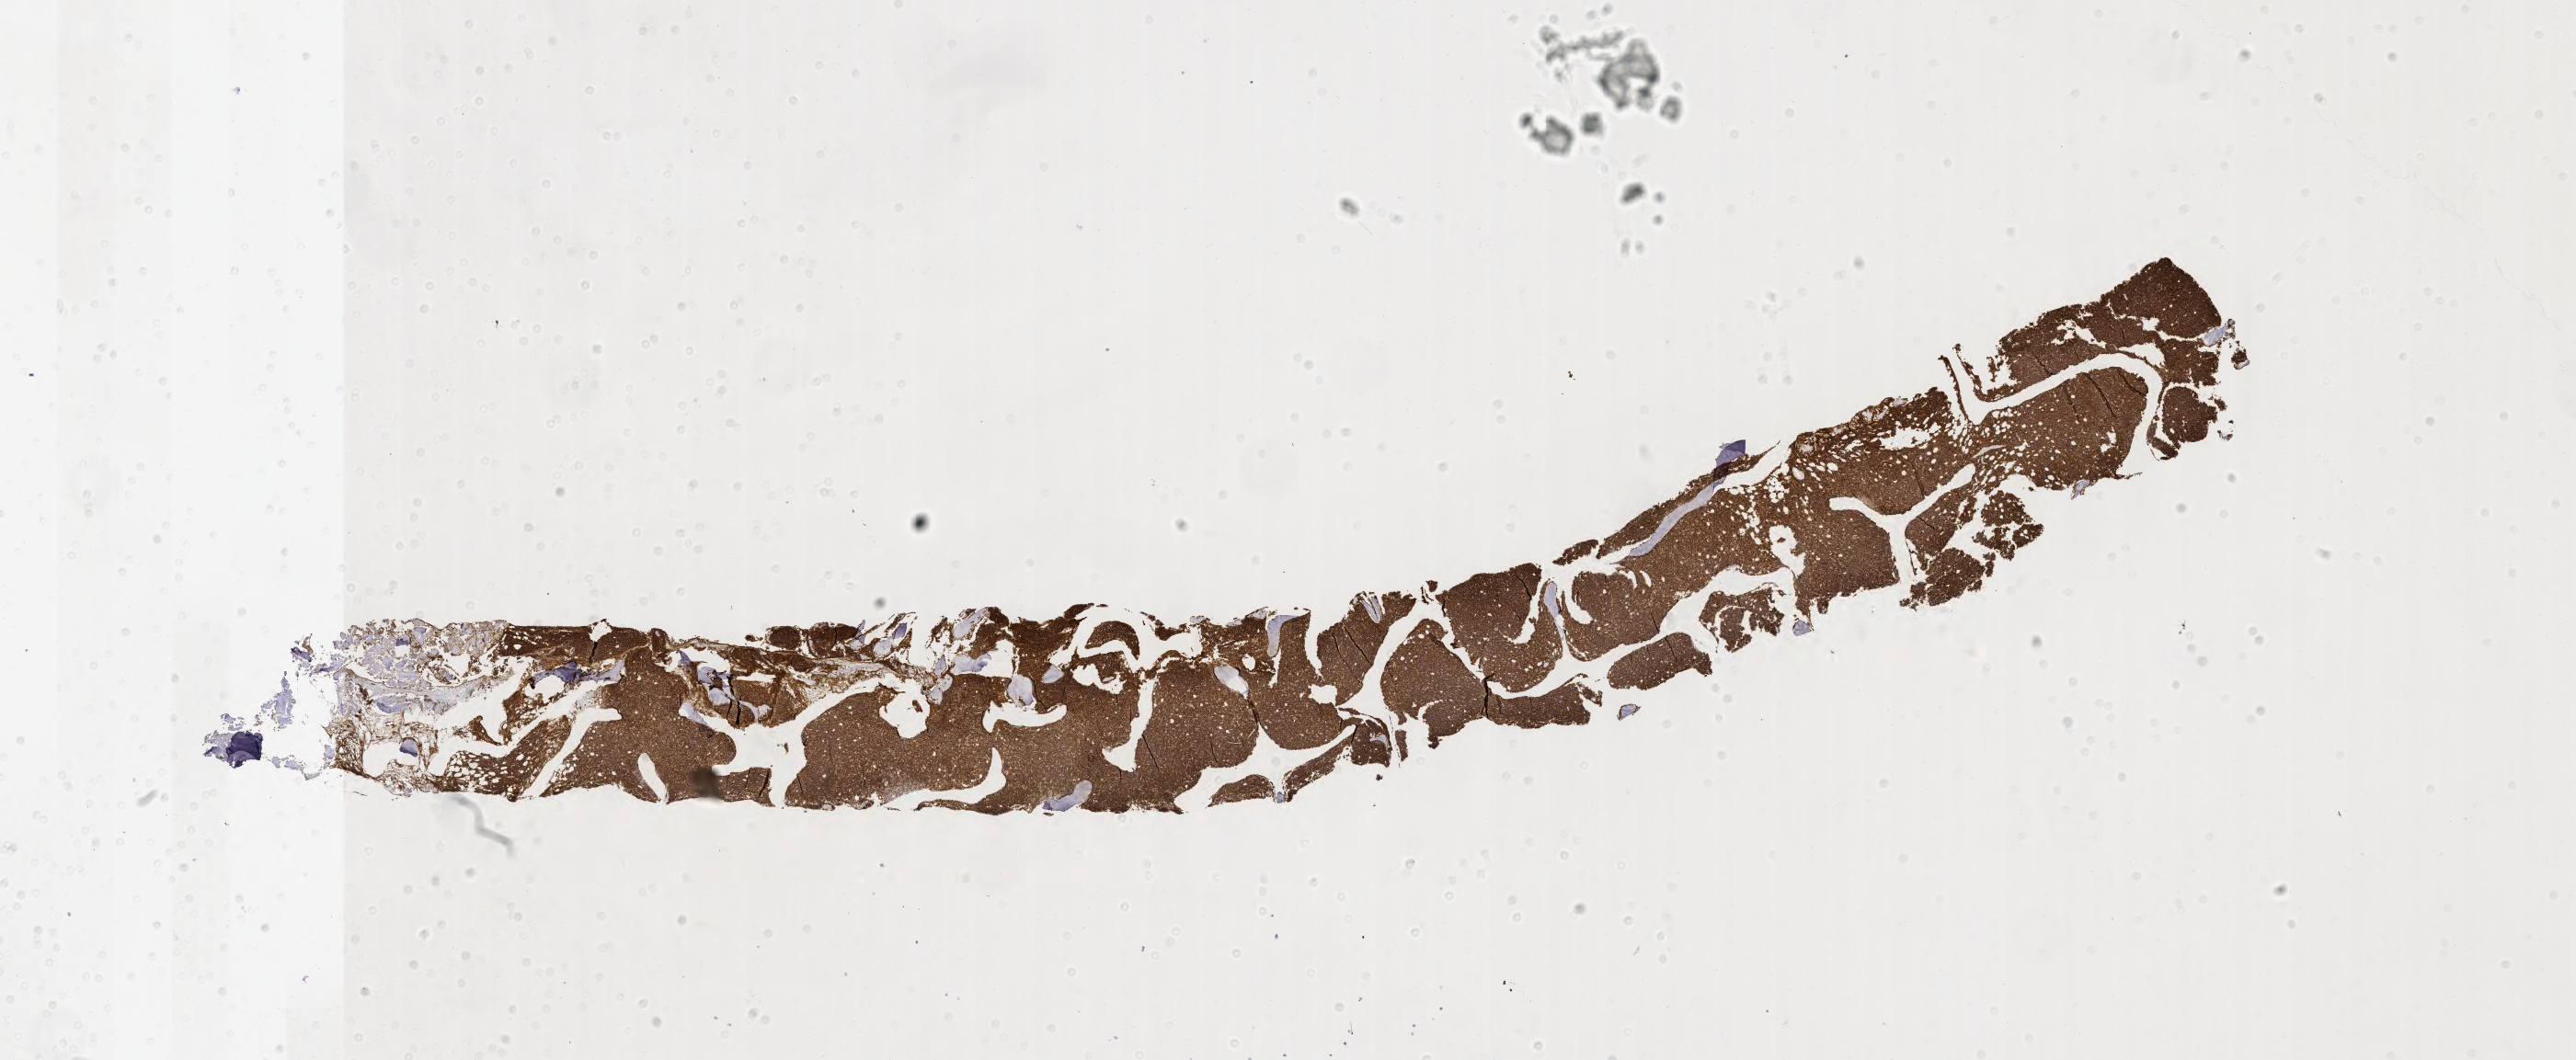
IHC for CD20, whole-slide image — shown as a low-resolution overview of the whole scanned area (about 22.6 x 9.3 mm). Specimen: tumor tissue. Patient sex: male.
Diagnosis: Burkitt lymphoma, NOS.